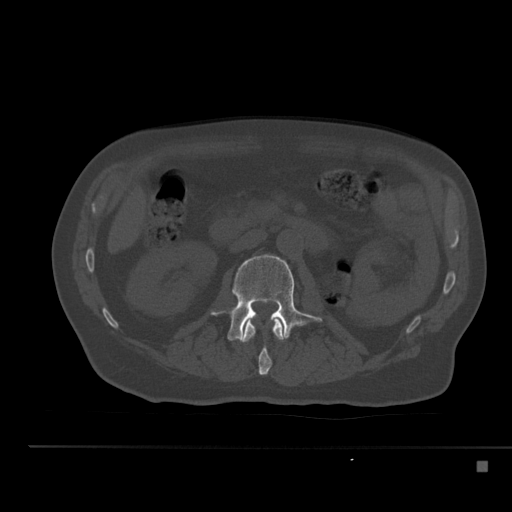
CT including the spine, one axial slice. Slice 191 of 517 in the series (ordered by position). Reconstruction kernel Br40s. Bone window (W 1800 / L 400 HU). 1.5 mm slice thickness. 512 × 512 image matrix. Male patient, age 70 years. Case-level facts recorded for this patient, not image findings: primary cancer: renal; vertebrae with lytic lesions (as recorded): T4, T6, T10, T12, L3, L4, L5.
Structures marked on this image (semi-automatically segmented with operator editing):
- L1 vertebra: bounding box (x1, y1, x2, y2) in pixels: (240, 318, 287, 375)
- L2 vertebra: (211, 254, 322, 341)